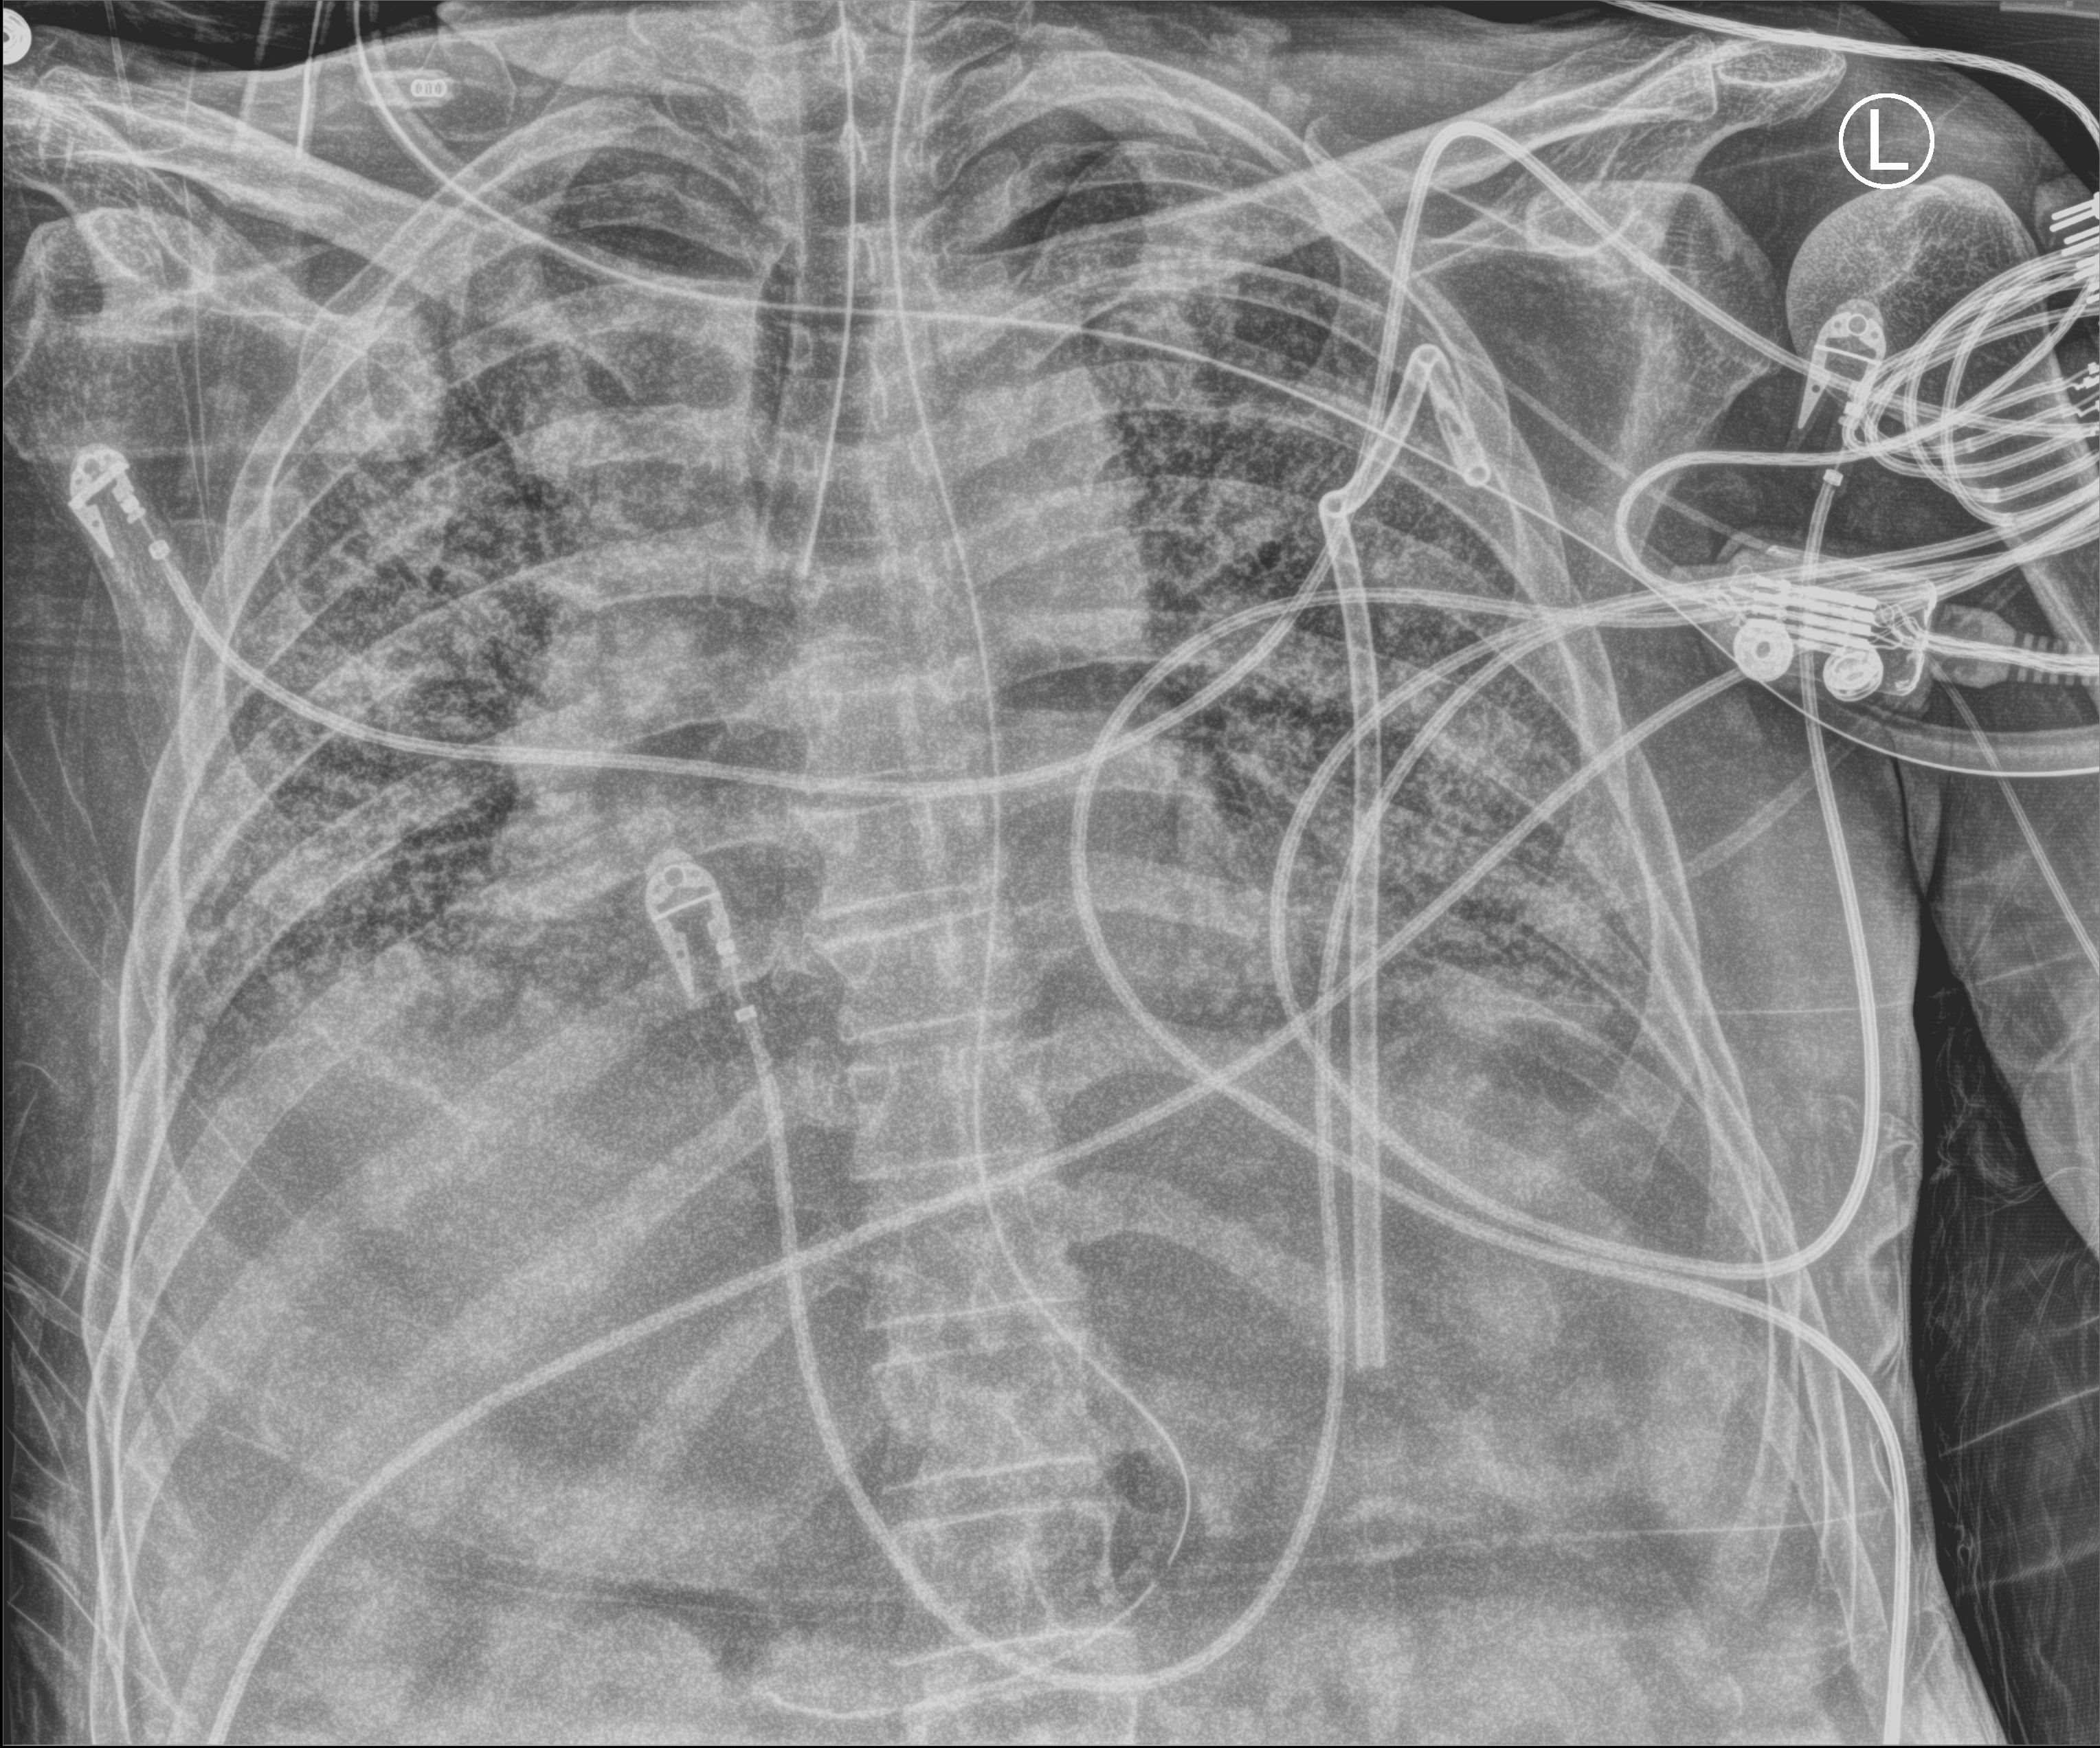
Chest X-ray (portable), anteroposterior (AP) projection. Patient hospitalised with COVID-19; male, aged 60–74 years.
Admission-level facts for this patient (not findings on this image; timing relative to this image not recorded):
- admitted to intensive care during this hospital stay: yes